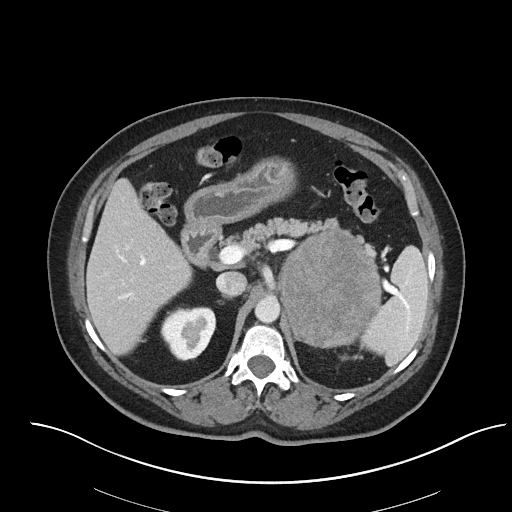
Contrast-enhanced abdominal CT, one axial slice; position 50 of 92 along the scan axis; reconstruction kernel I40f/2; 120 kVp; soft-tissue window (W 400 / L 40 HU); 3 mm slice thickness; 512 × 512 image matrix. Female patient, age 53 years. Case-level facts recorded for this patient, not image findings: diagnosis: adrenocortical carcinoma; tumour side: left adrenal; tumour size at pathology: 9 cm; Ki-67 index: 28 %; stage (as recorded): 2.
Structures marked on this image (semi-automatic segmentation, software-assisted and operator-edited):
- mass: bounding box (x1, y1, x2, y2) in pixels: (281, 232, 380, 346)